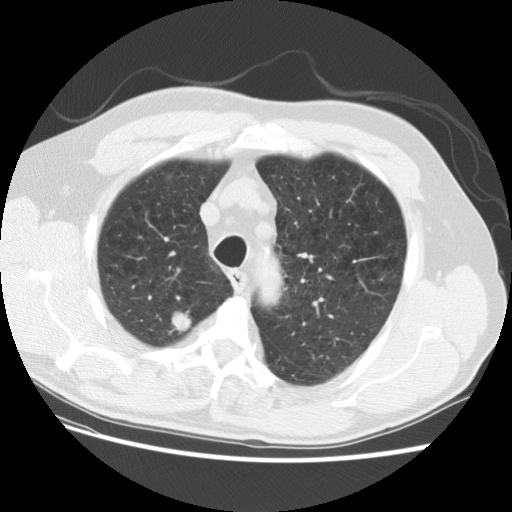
Low-dose screening chest CT, one axial slice; position 99 of 124 along the scan axis; lung window (W 1500 / L -600 HU); 2.5 mm slice thickness; 512 × 512 image matrix, field of view 361 × 361 mm.
Annotated regions visible in this slice (outlined manually by an expert reader):
- lesion 1 (tumor, upper lobe of right lung): bounding box [x1, y1, x2, y2] px = [172, 312, 192, 333]